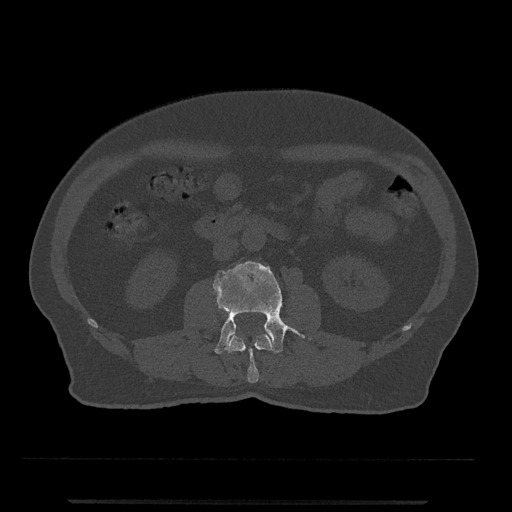
CT including the spine, one axial slice; slice 226 of 797 in the series (ordered by position); 120 kVp; bone window (W 1800 / L 400 HU); 0.5 mm slice thickness; 512 × 512 image matrix, field of view 419 × 419 mm. Male patient, age 63 years. From the clinical record (not read from this slice): primary cancer: prostate.
Outlined on this slice (semi-automatic segmentation, software-assisted and operator-edited):
- L2 vertebra: bounding box (x1, y1, x2, y2) in pixels: (227, 333, 275, 383)
- L3 vertebra: (213, 261, 311, 354)